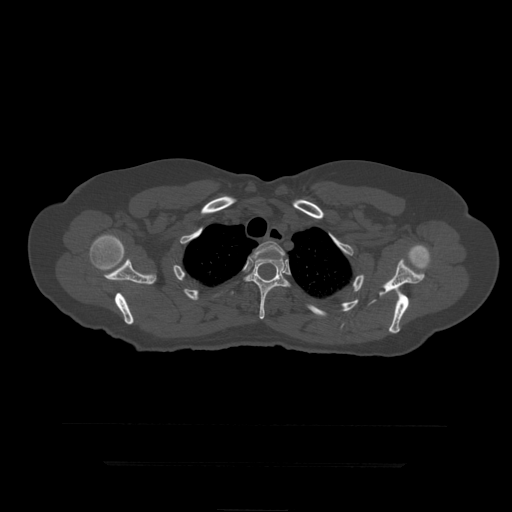
CT including the spine, one axial slice; position 352 of 399 along the scan axis; 120 kVp; bone window (W 1800 / L 400 HU); 1.25 mm slice thickness; 512 × 512 image matrix, field of view 450 × 450 mm. Patient age 41 years. Case-level facts recorded for this patient, not image findings: primary cancer: breast.
Annotated regions visible in this slice (semi-automatic segmentation, software-assisted and operator-edited):
- T3 vertebra: bounding box <251,241,286,259> (left, top, right, bottom; pixels)
- T4 vertebra: <244,256,291,320>